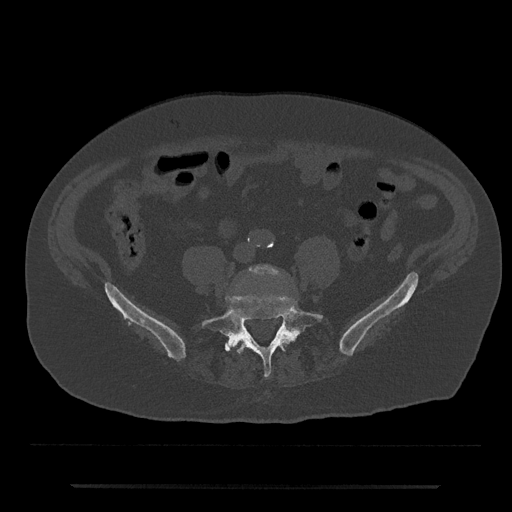
CT including the spine, one axial slice; reconstruction kernel Br40s/3; bone window (W 1800 / L 400 HU); 0.5 mm slice thickness; 512 × 512 image matrix, field of view 434 × 434 mm. Patient: male, 80 years. From the clinical record (not read from this slice): primary cancer: prostate.
Structures marked on this image (semi-automatically segmented with operator editing):
- L4 vertebra: bounding box <248,265,280,276> (left, top, right, bottom; pixels)
- L5 vertebra: <201,295,323,377>